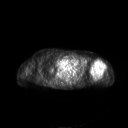
FDG PET of an extremity soft-tissue mass (from a PET/CT study), one axial slice; 3.27 mm slice thickness; 128 × 128 image matrix, field of view 700 × 700 mm. Female patient, age 83 years. From the clinical record (not read from this slice): histological type: pleiomorphic leiomyosarcoma; grade: high; site of the primary tumour: left biceps.
Outlined on this slice (expert contour drawn on MRI and transferred to this co-registered scan by the dataset authors):
- gross tumour volume including surrounding oedema: bounding box <90,60,106,77> (left, top, right, bottom; pixels)
- gross tumour volume (mass): <90,60,105,77>